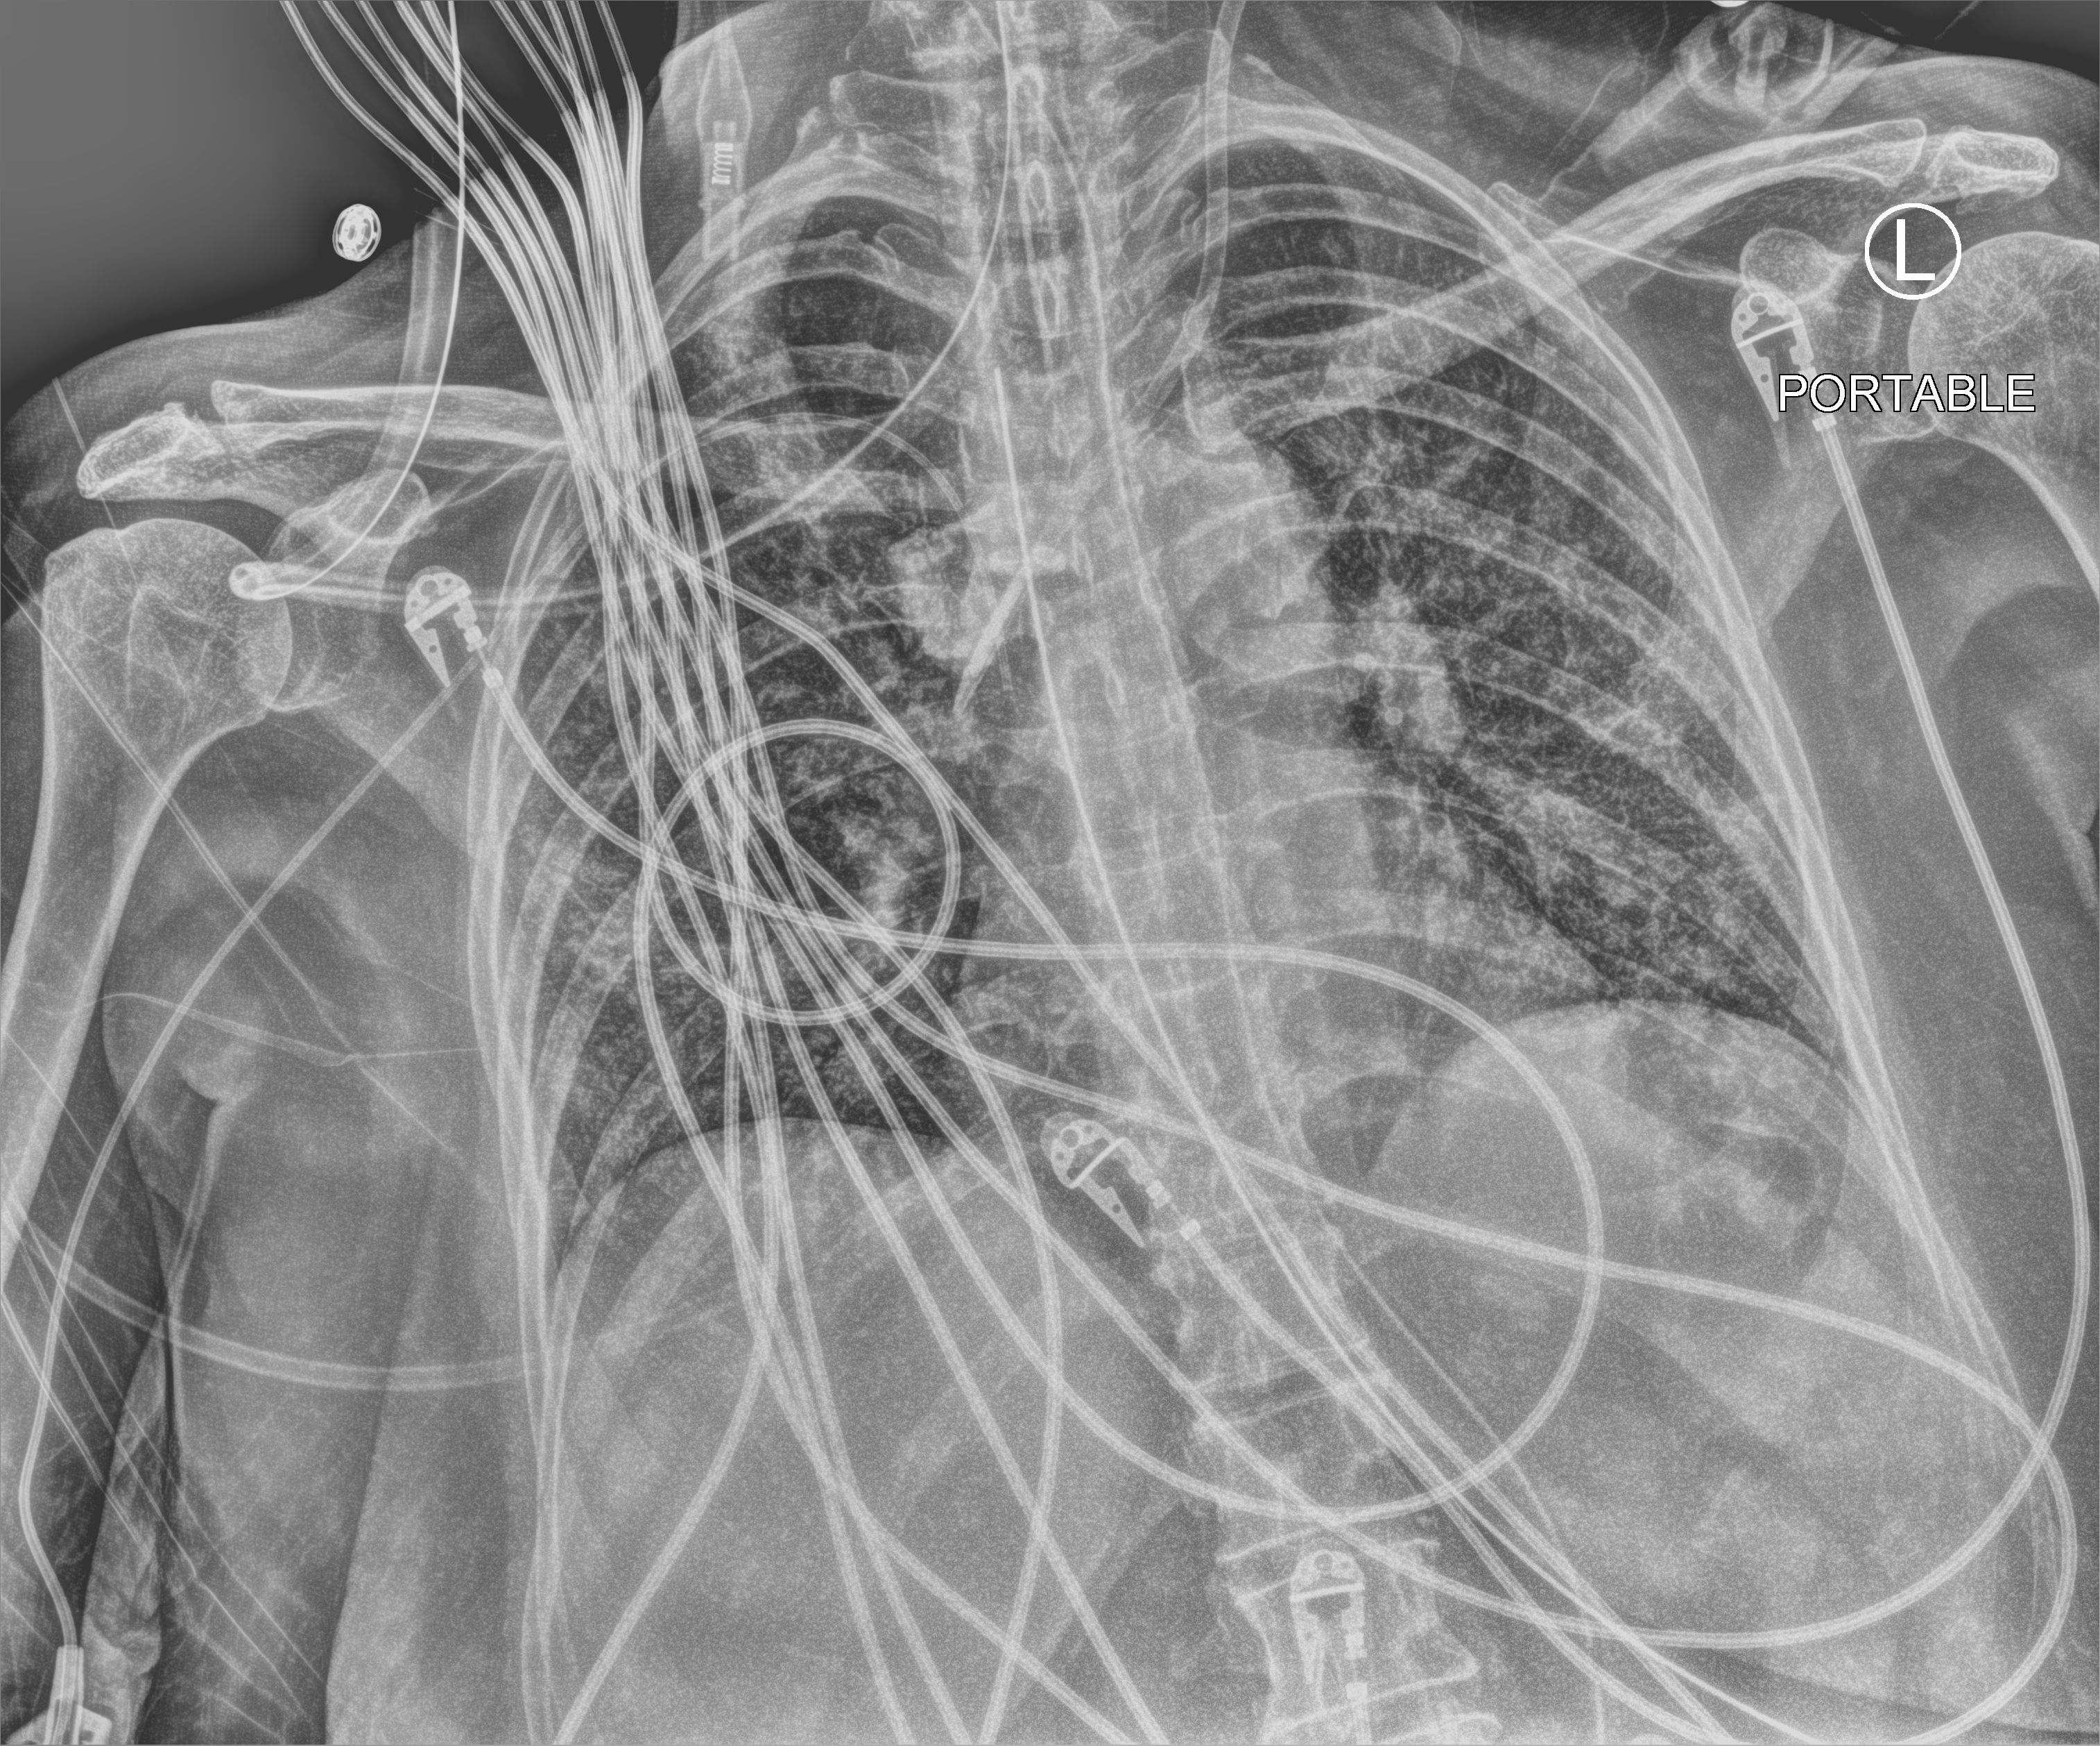
Bedside chest radiograph (computed radiography); anteroposterior (AP) projection. Female patient hospitalised with COVID-19, age 60–74 years.
Hospital-stay facts (about this admission, not read from this image; timing relative to this image not recorded): admitted to intensive care during this hospital stay: yes; mechanically ventilated during this hospital stay: yes.